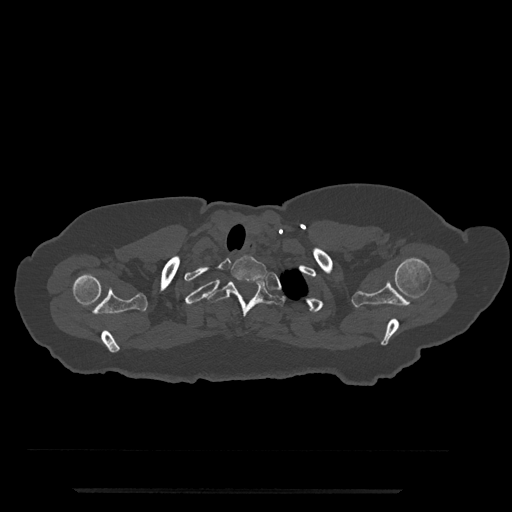
CT including the spine, one axial slice; position 686 of 797 along the scan axis; reconstruction kernel Br40s/3; bone window (W 1800 / L 400 HU); 0.5 mm slice thickness; 512 × 512 image matrix. Patient: female, 51 years. Case-level facts recorded for this patient, not image findings: primary cancer: neuro; vertebrae with lytic lesions (as recorded): T8.
Structures marked on this image (semi-automatic segmentation, software-assisted and operator-edited):
- T1 vertebra: bounding box <231,255,267,282> (left, top, right, bottom; pixels)
- T2 vertebra: <206,274,285,317>